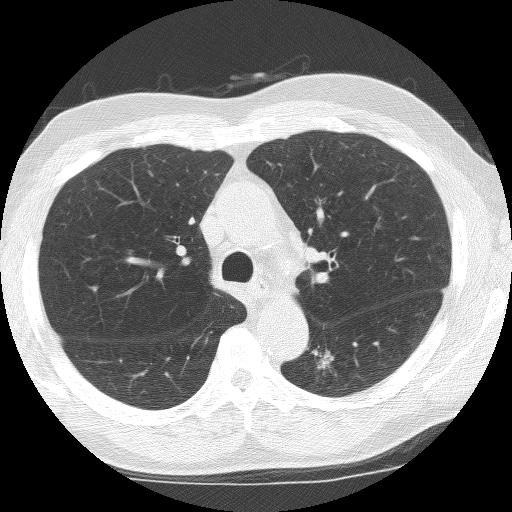
Low-dose screening chest CT, one axial slice. Position 102 of 155 along the scan axis. 120 kVp. Lung window (W 1500 / L -600 HU). 2.5 mm slice thickness. 512 × 512 image matrix.
Annotated regions visible in this slice (outlined manually by an expert reader):
- lesion 1 (tumor, lower lobe of left lung): bounding box <313,346,334,370> (left, top, right, bottom; pixels)